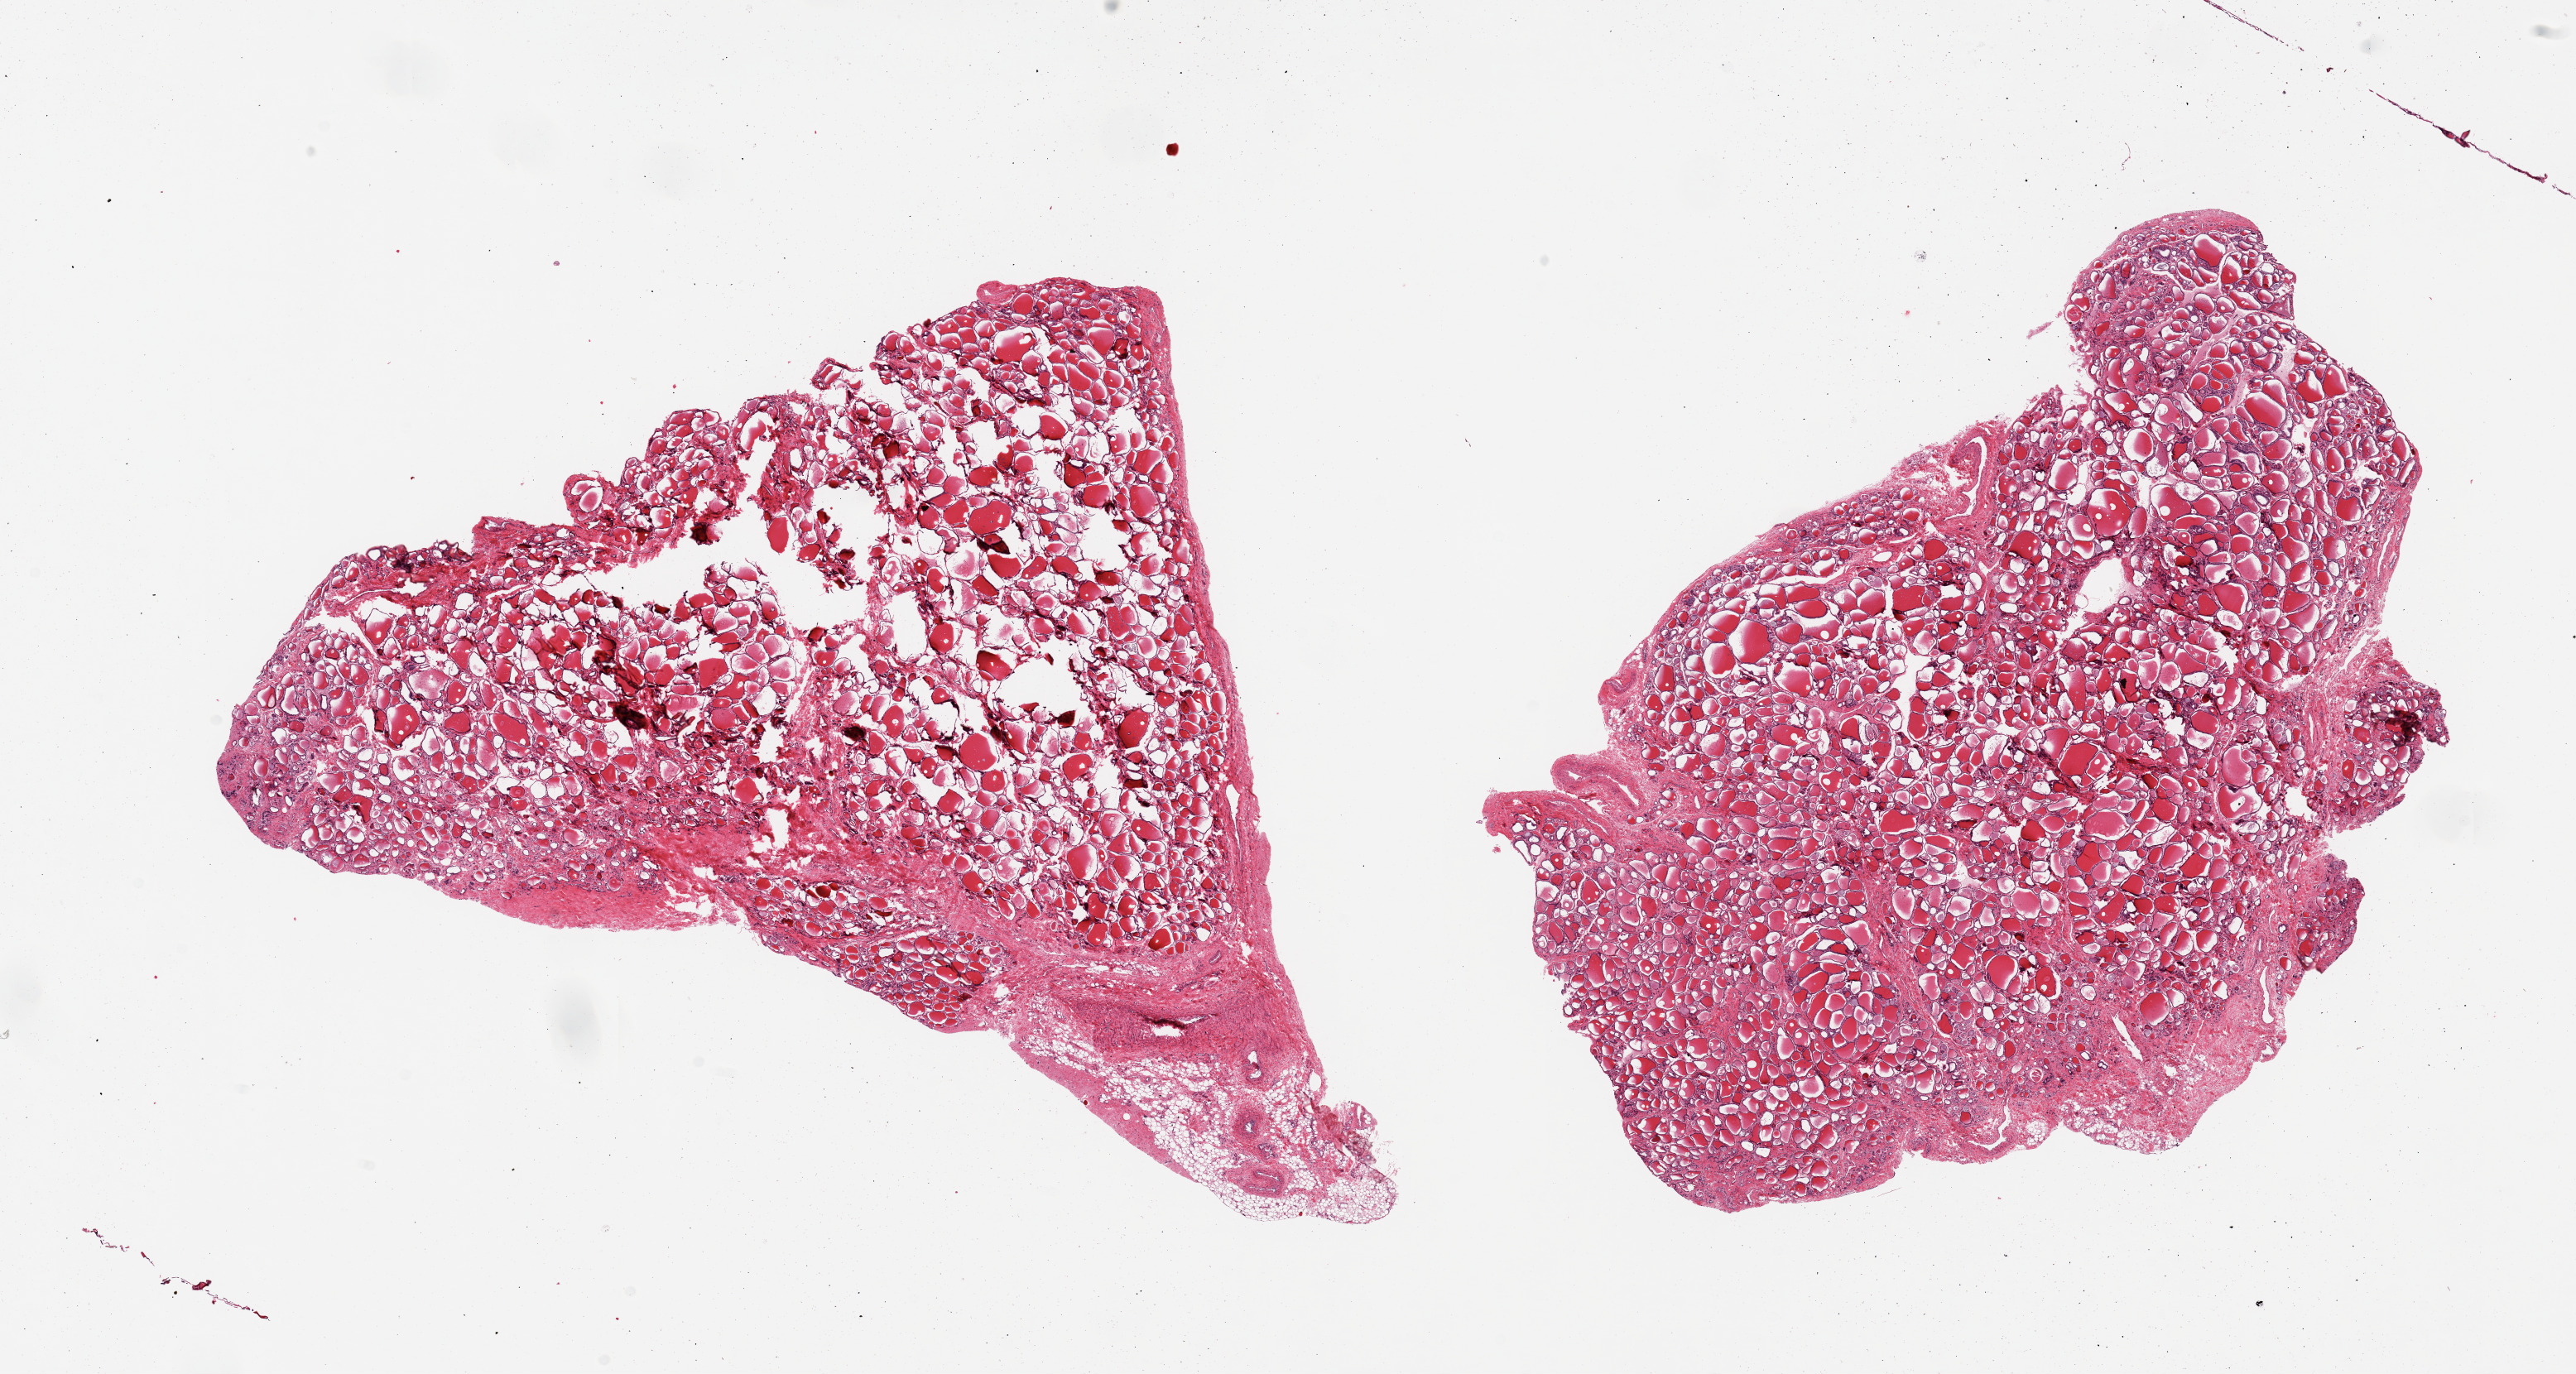
Haematoxylin and eosin whole-slide image — low-resolution overview of the scanned area, about 24.6 x 13.1 mm. PAXgene-fixed, paraffin-embedded tissue. Target tissue: thyroid. Tissue donor sample. Donor sex: male.
Review note (as recorded): 2 pieces; 10% fibrofatty portion on 1 edge.